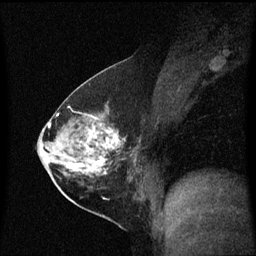
Breast MRI (dynamic contrast-enhanced), one sagittal slice. Position 30 of 60 along the scan axis. Dynamic contrast-enhanced series, image 2 of 3 at this slice position (ordered by acquisition). 1.5 T. TE 4.2 ms, TR 8.4 ms. 256 × 256 image matrix. Patient: female, 54 years. From the clinical record (not read from this slice): setting: breast cancer imaged before/during neoadjuvant chemotherapy; receptor status: HER2-positive.
Structures marked on this image (semi-automatic segmentation, software-assisted and operator-edited):
- analysis volume of interest (the breast-tissue region the enhancement analysis was run in; not a lesion): bounding box [x1, y1, x2, y2] px = [59, 115, 140, 199]
- tumour enhancement mask (voxels above the 70 % enhancement threshold inside the analysis volume of interest): [66, 126, 120, 174]